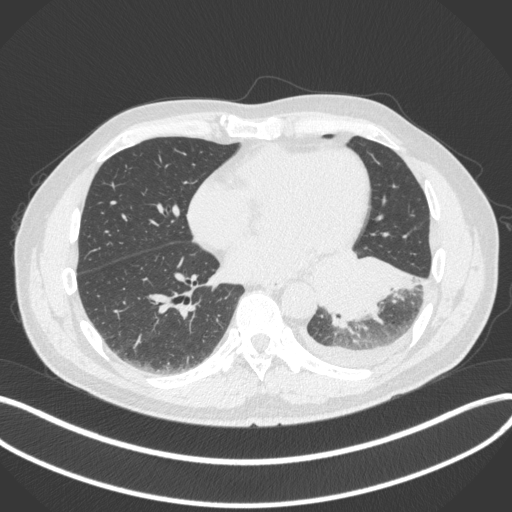
Chest CT, one axial slice; slice 142 of 350 in the series (ordered by position); reconstruction kernel B31f; lung window (W 1500 / L -600 HU); 1 mm slice thickness; 512 × 512 image matrix, field of view 400 × 400 mm. Patient: male, 58 years. Case-level facts recorded for this patient, not image findings: clinical TNM (as recorded): T3 N1 M1b.
Outlined on this slice (bounding box drawn by a radiologist):
- lung tumour (recorded histology: small cell carcinoma): bounding box [x1, y1, x2, y2] px = [312, 256, 432, 328]